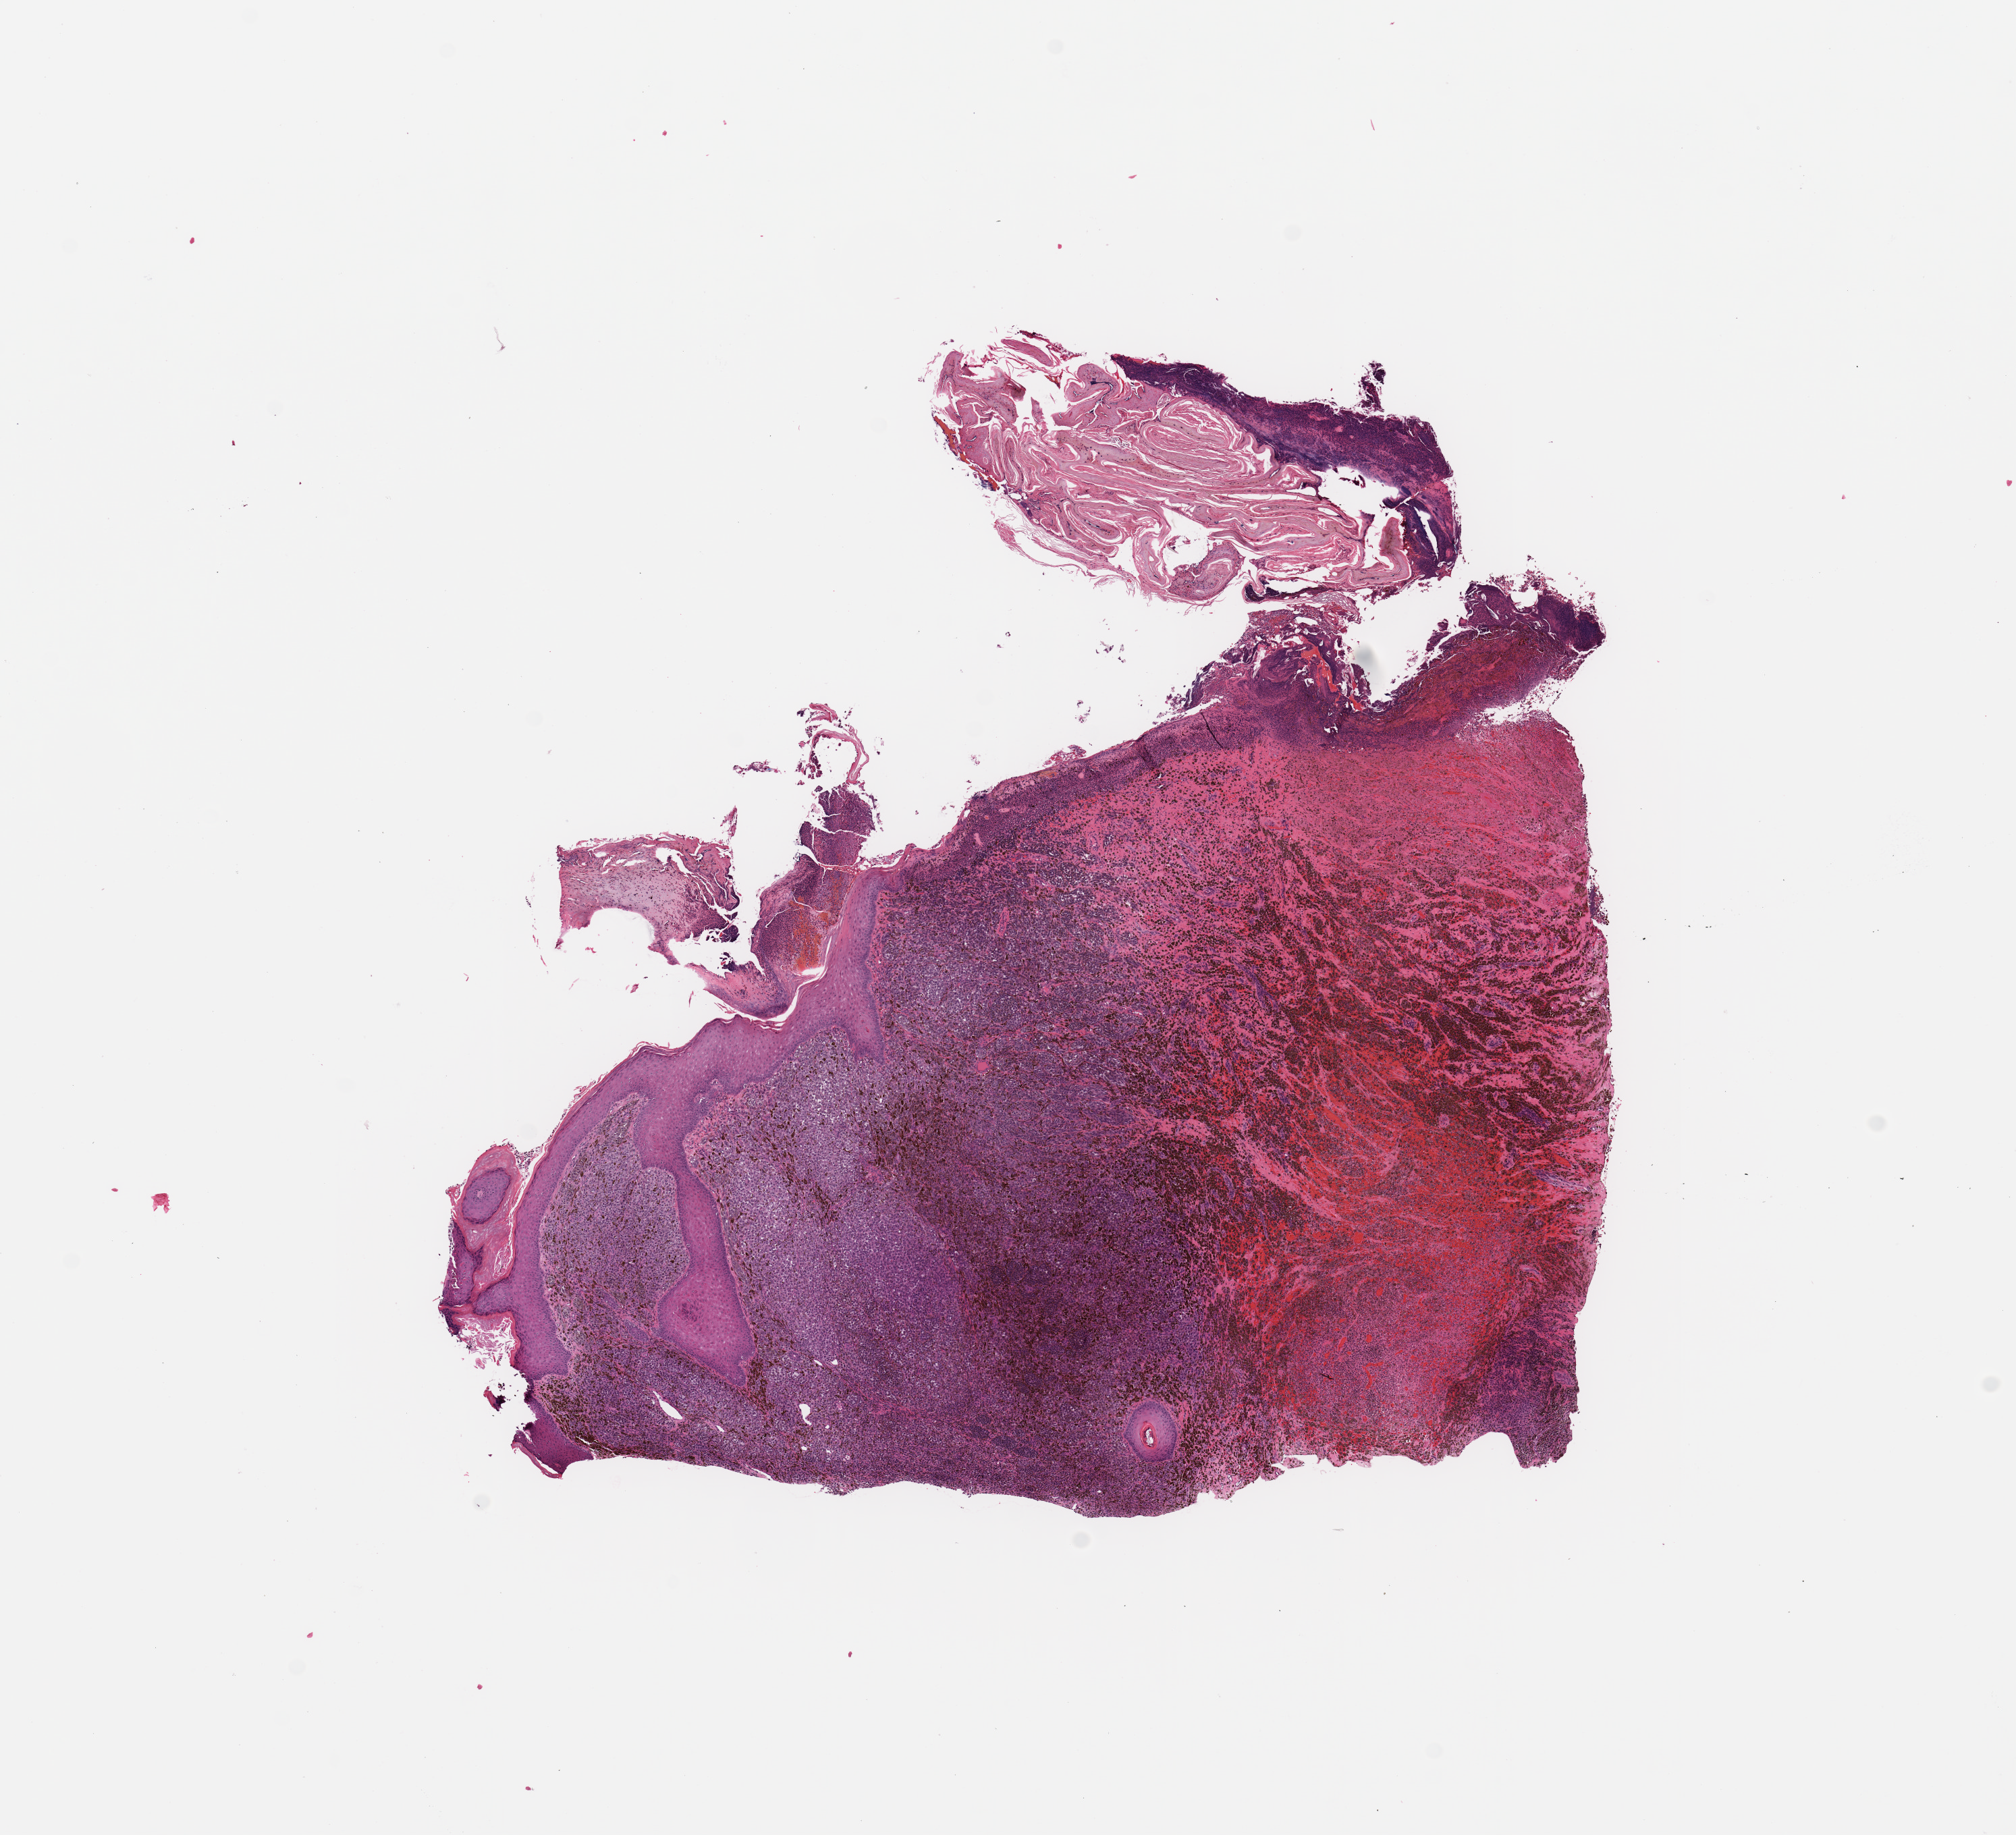
Digitized H&E-stained tissue section (whole slide) — low-resolution overview of the scanned area, about 11.8 x 10.8 mm, melanoma tumour tissue; sampled site not recorded. 69-year-old female patient.
Primary tumour site (as recorded): trunk. Histologic diagnosis: Malignant melanoma, NOS. AJCC pathologic stage: IIIB.